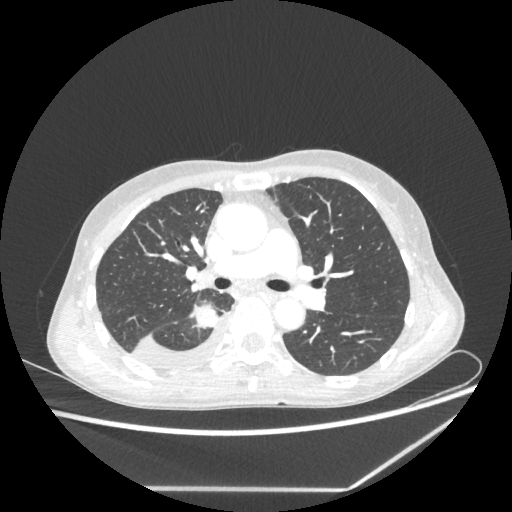
Chest CT, one axial slice; slice 140 of 237 in the series (ordered by position); reconstruction kernel STANDARD; lung window (W 1500 / L -600 HU); 1.25 mm slice thickness; 512 × 512 image matrix, field of view 364 × 364 mm. Female patient, age 59 years. From the clinical record (not read from this slice): clinical TNM (as recorded): T1c N1 M1.
Structures marked on this image (bounding box drawn by a radiologist):
- lung tumour (recorded histology: adenocarcinoma): box from (x=189, y=300) to (x=220, y=330) px